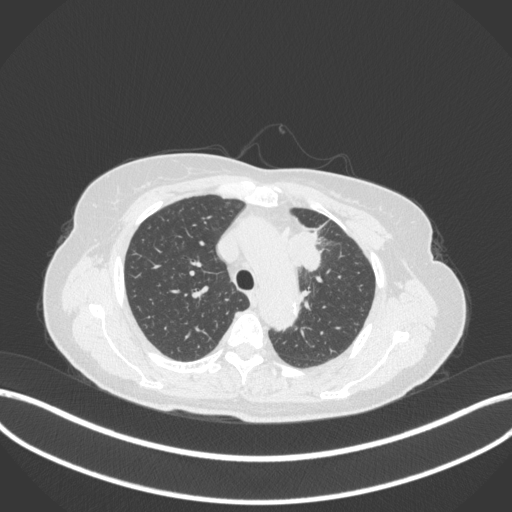
Chest CT, one axial slice; slice 247 of 368 in the series (ordered by position); reconstruction kernel B31f; 120 kVp; lung window (W 1500 / L -600 HU); 512 × 512 image matrix, field of view 400 × 400 mm. Patient: female, 65 years. From the clinical record (not read from this slice): clinical TNM (as recorded): T2a N0 M0; histopathological grade: G2-3.
Outlined on this slice (bounding box drawn by a radiologist):
- lung tumour (recorded histology: adenocarcinoma): bounding box [x1, y1, x2, y2] px = [285, 227, 325, 273]